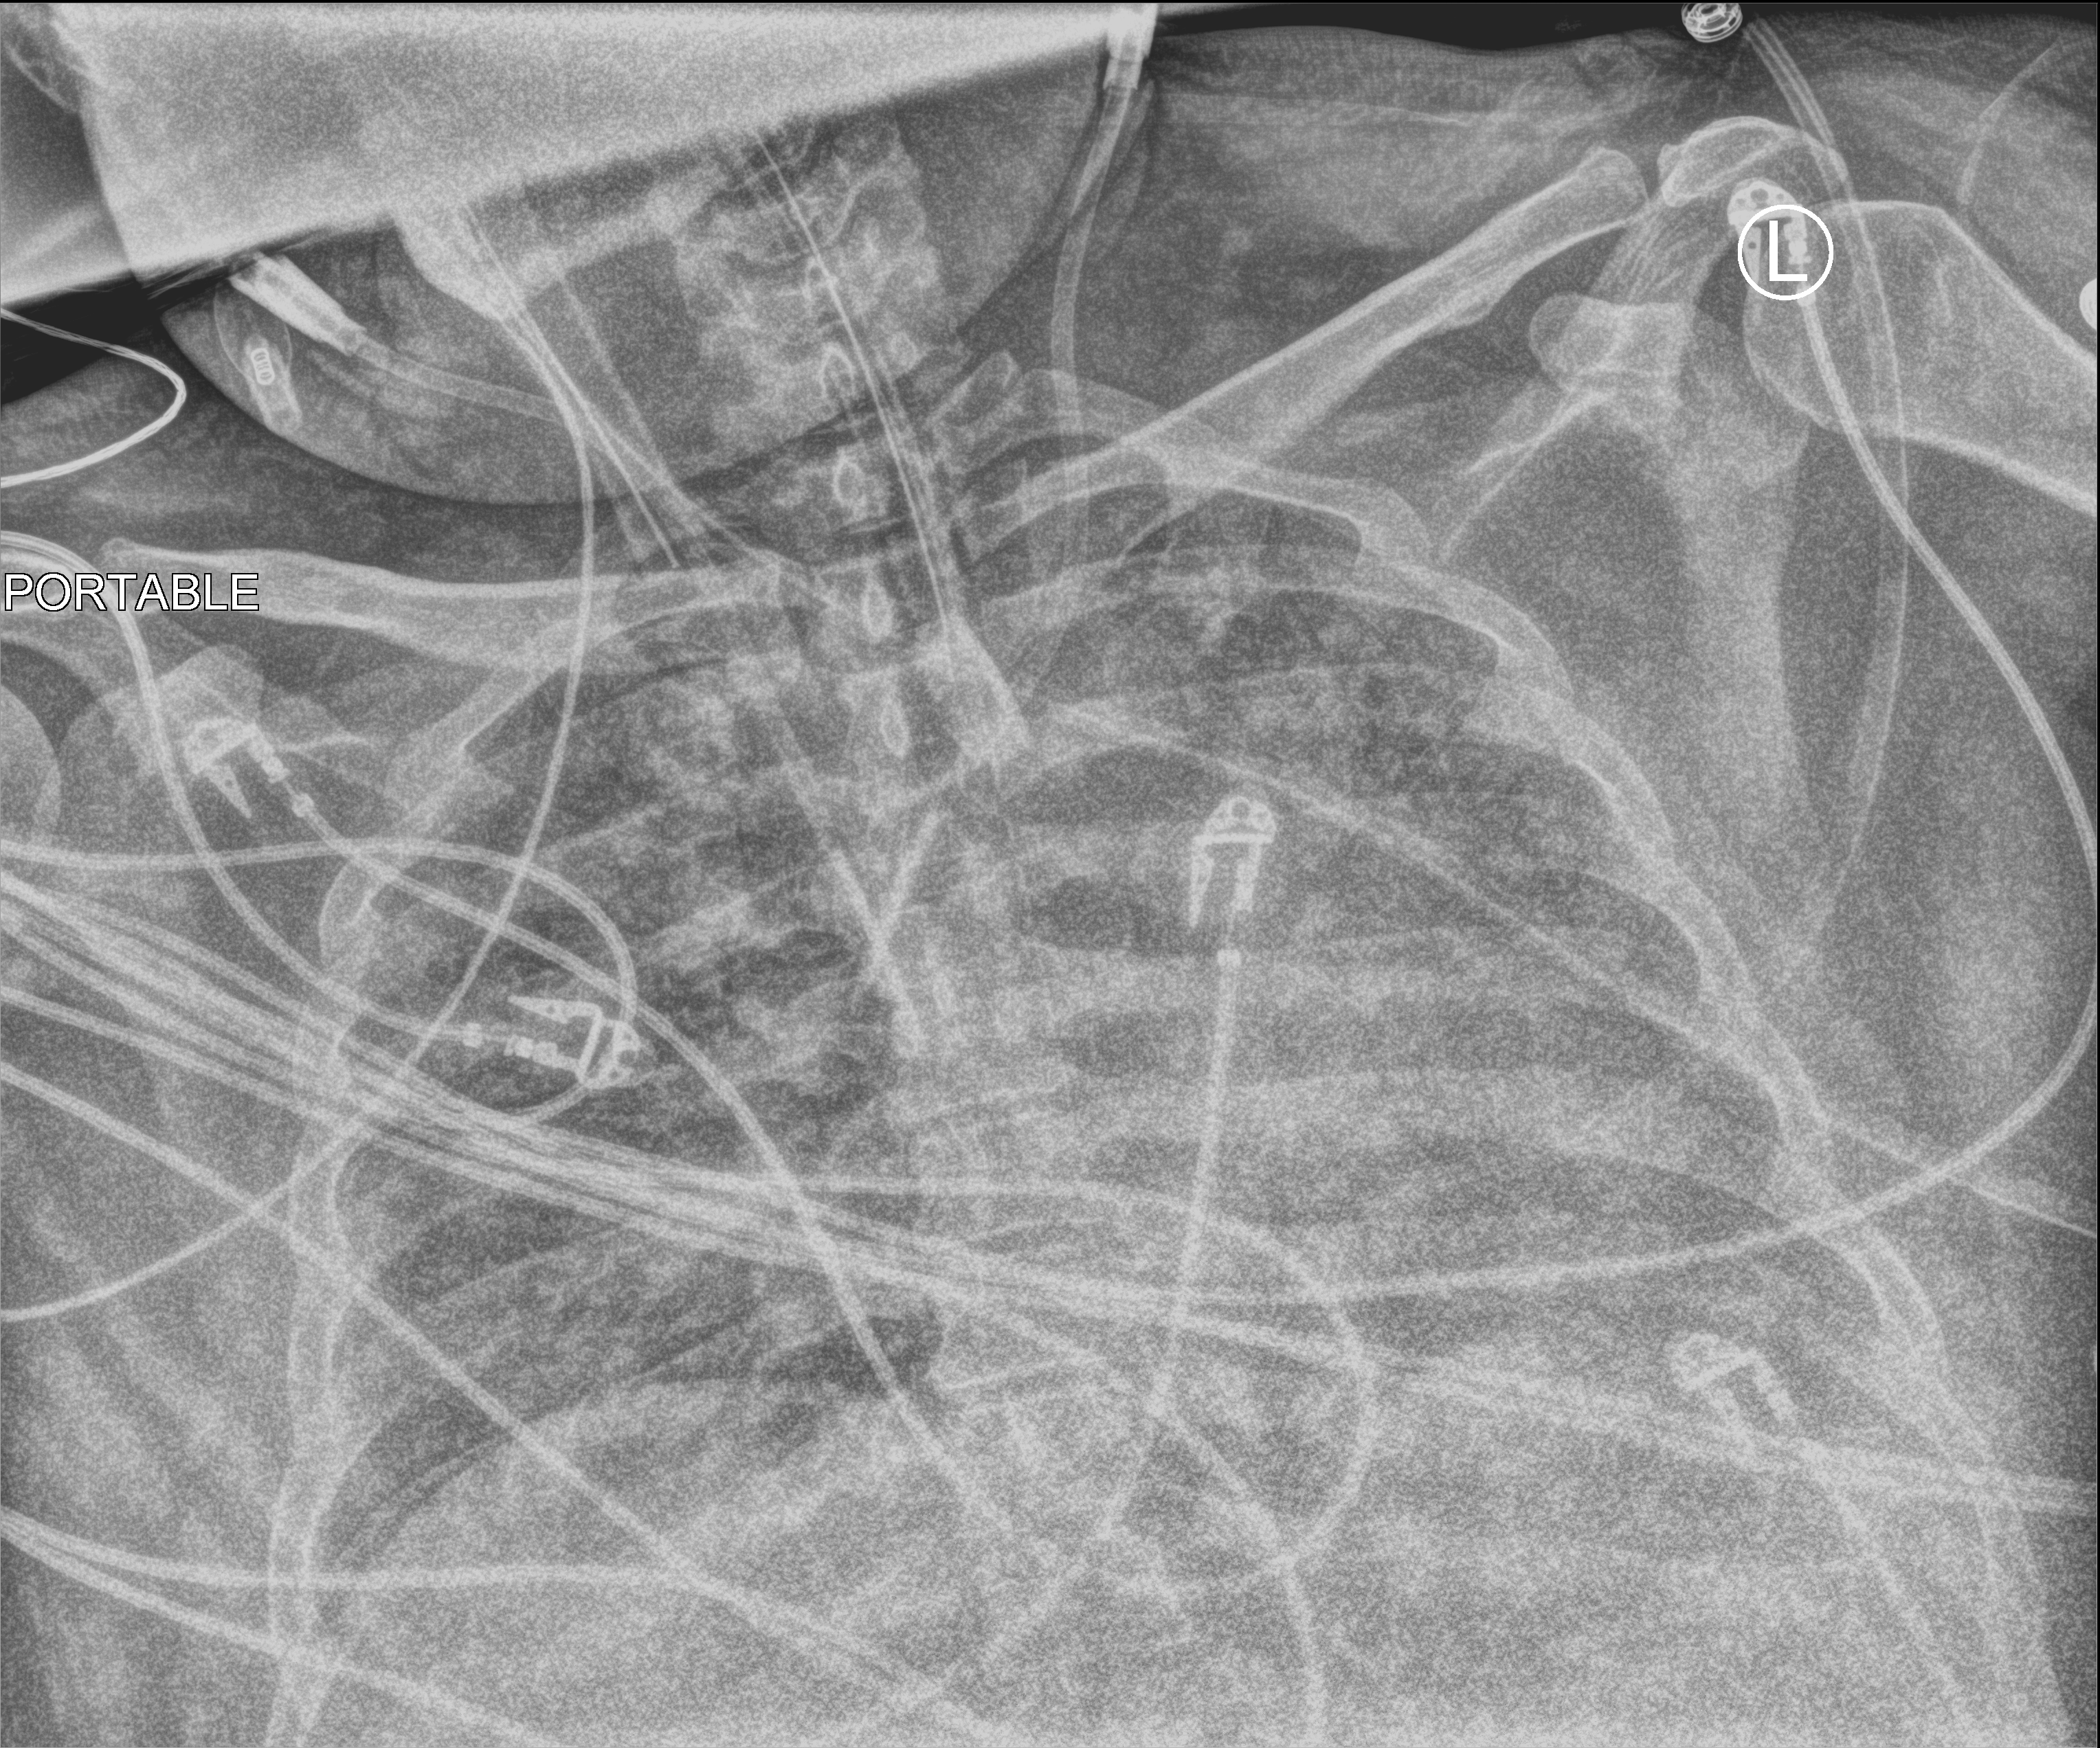
Chest X-ray (portable), anteroposterior (AP) projection. Adult patient hospitalised with COVID-19, age 18–59 years.
From the hospital-stay record, not from the radiograph (when in the stay this image was taken is not recorded):
- mechanically ventilated during this hospital stay: yes
- length of hospital stay: 22 days
- admitted to intensive care during this hospital stay: yes